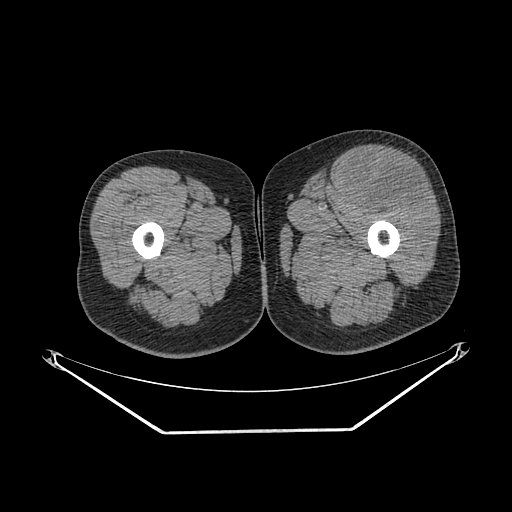
CT of an extremity soft-tissue mass (from a PET/CT study), one axial slice. Position 241 of 267 along the scan axis. Soft-tissue window (W 400 / L 40 HU). 3.75 mm slice thickness. 512 × 512 image matrix, field of view 500 × 500 mm. Male patient. From the clinical record (not read from this slice): histological type: extraskeletal osteosarcoma; grade: high; site of the primary tumour: thigh.
Annotated regions visible in this slice (expert contour drawn on MRI and transferred to this co-registered scan by the dataset authors):
- gross tumour volume (mass): box from (x=352, y=160) to (x=430, y=211) px